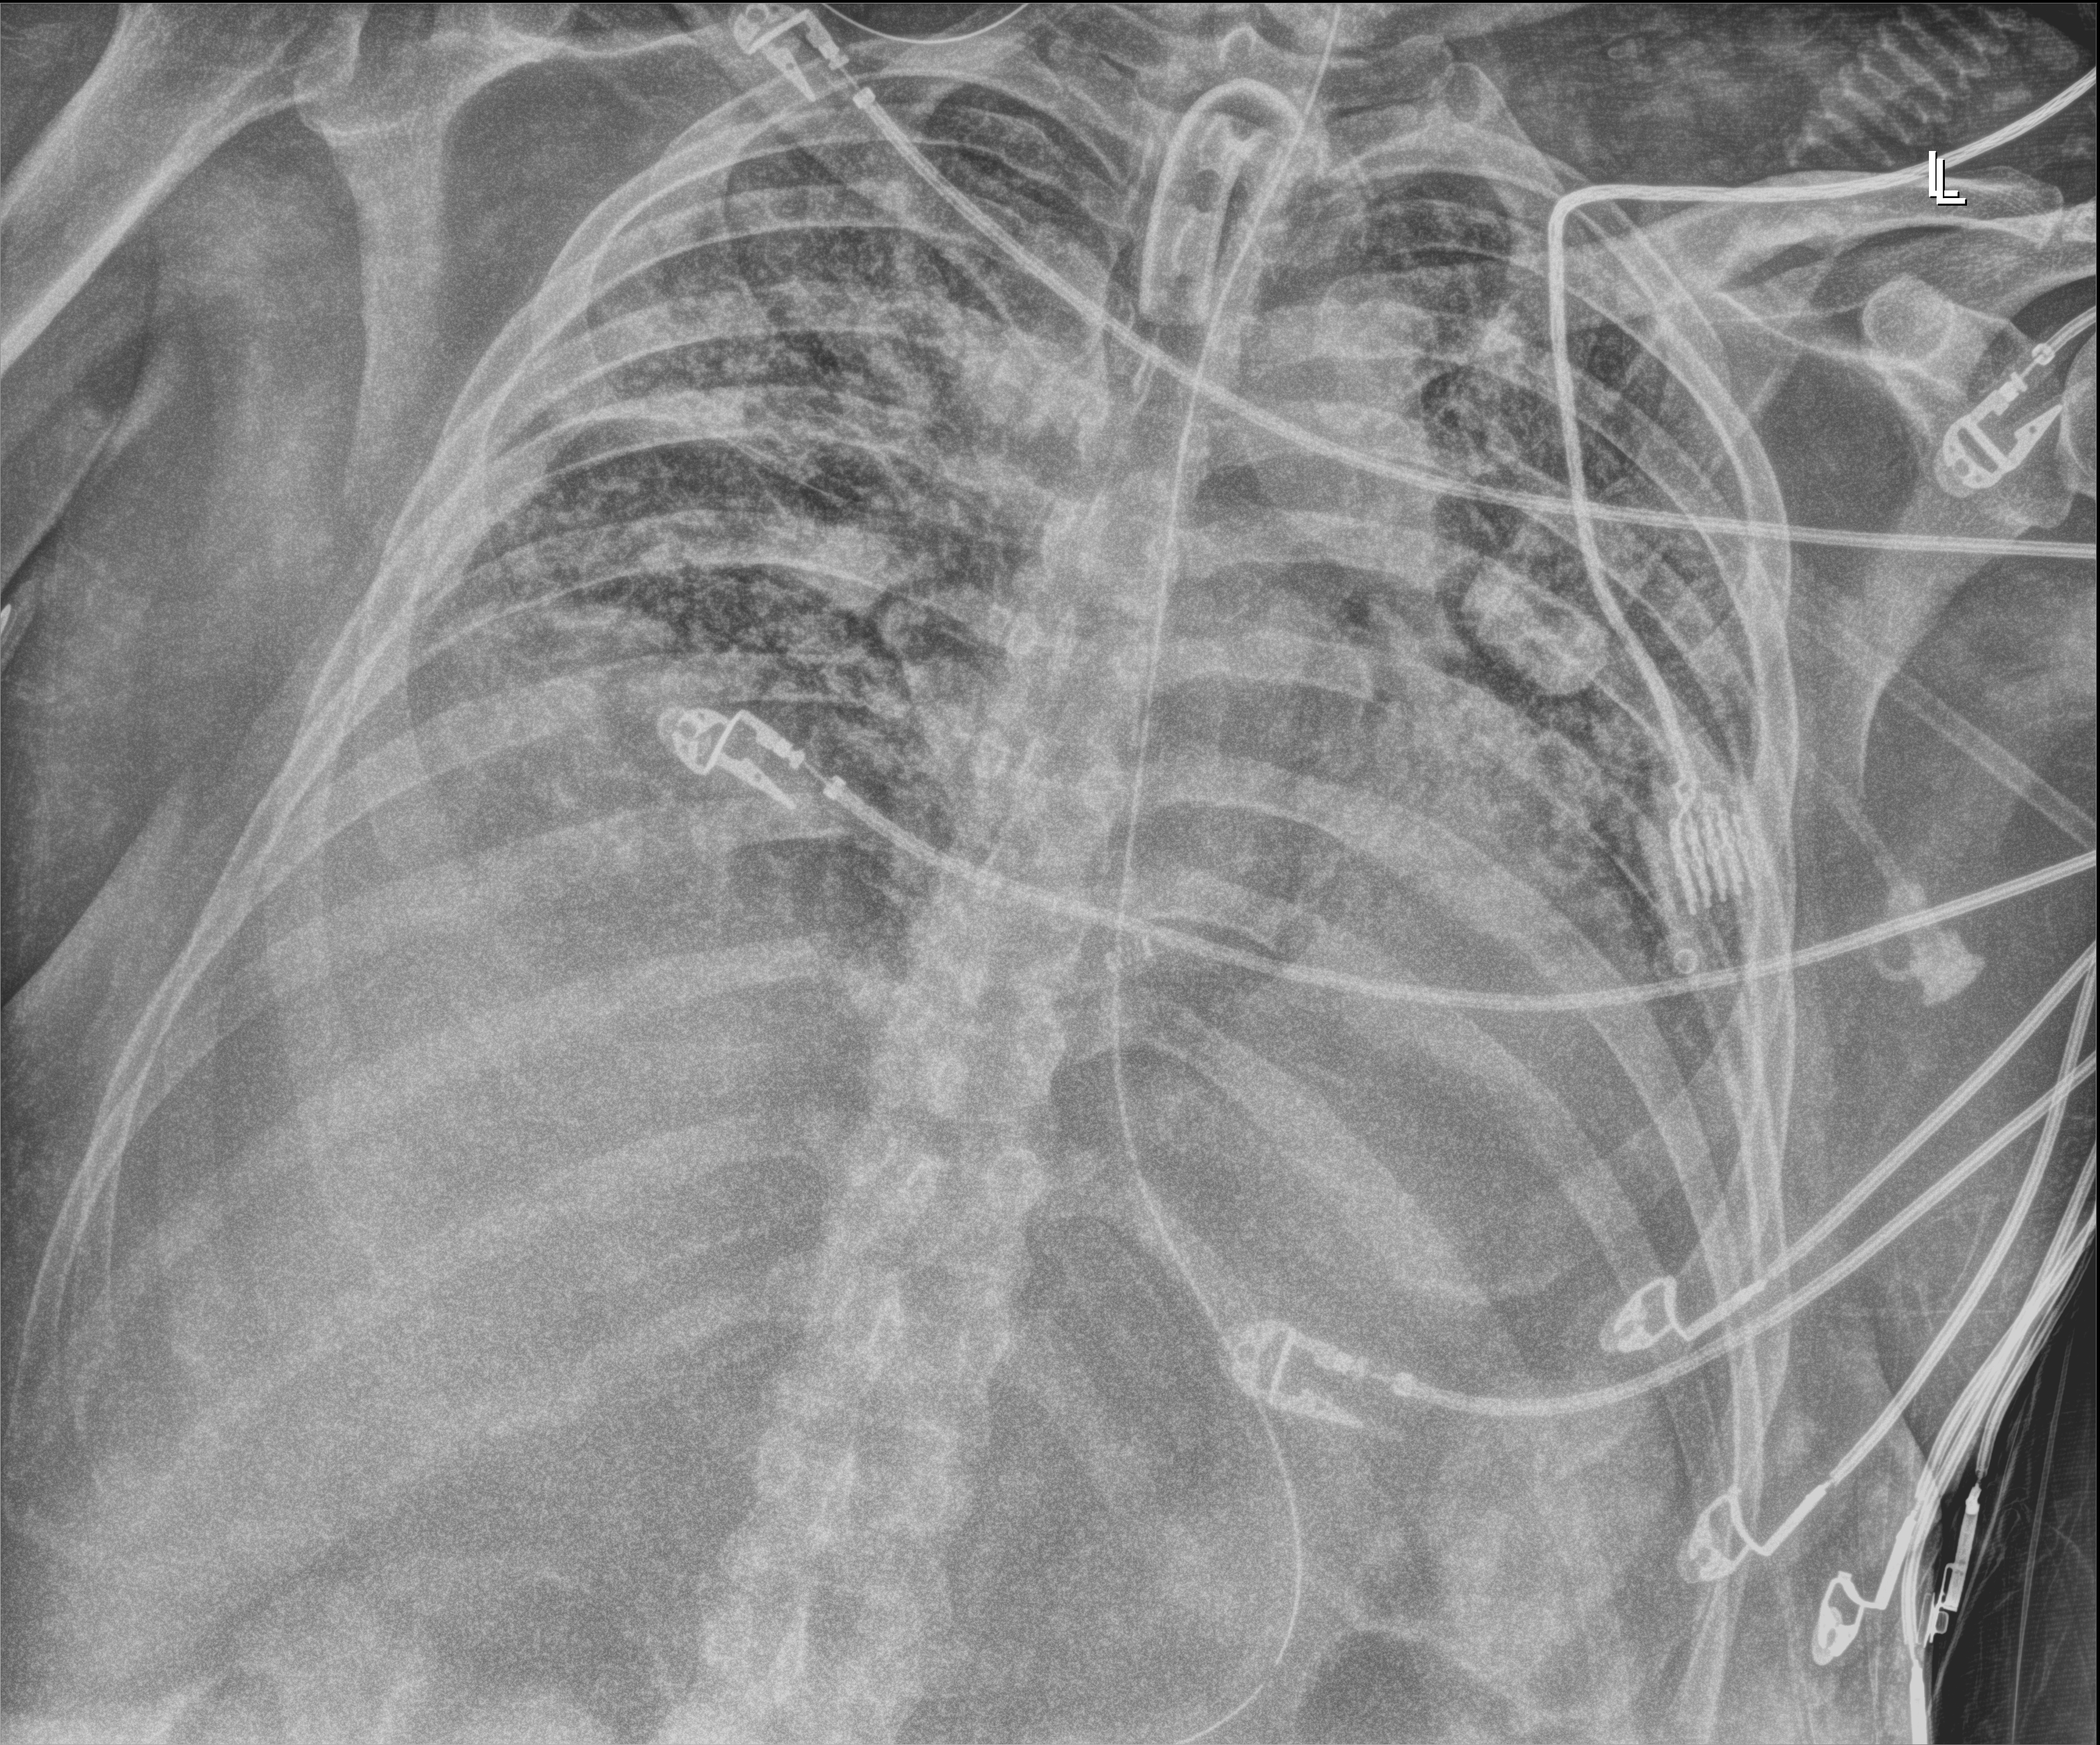
Chest X-ray (portable); anteroposterior (AP) projection. Patient hospitalised with COVID-19; male, aged 18–59 years.
From the hospital-stay record, not from the radiograph (when in the stay this image was taken is not recorded): diabetes (admission record): no.